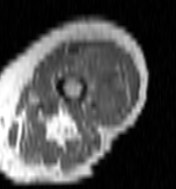
MRI of an extremity soft-tissue mass, one axial slice. Slice 37 of 100 in the series (ordered by position). MR volume resampled by the dataset authors to the PET/CT grid (not the native acquisition matrix). 176 × 189 image matrix. Female patient. From the clinical record (not read from this slice): histological type: undifferentiated – high grade; grade: high; site of the primary tumour: left thigh.
Structures marked on this image (expert contour drawn on MRI and transferred to this co-registered scan by the dataset authors):
- gross tumour volume including surrounding oedema: bounding box <62,46,127,122> (left, top, right, bottom; pixels)
- gross tumour volume (mass): <91,54,125,122>